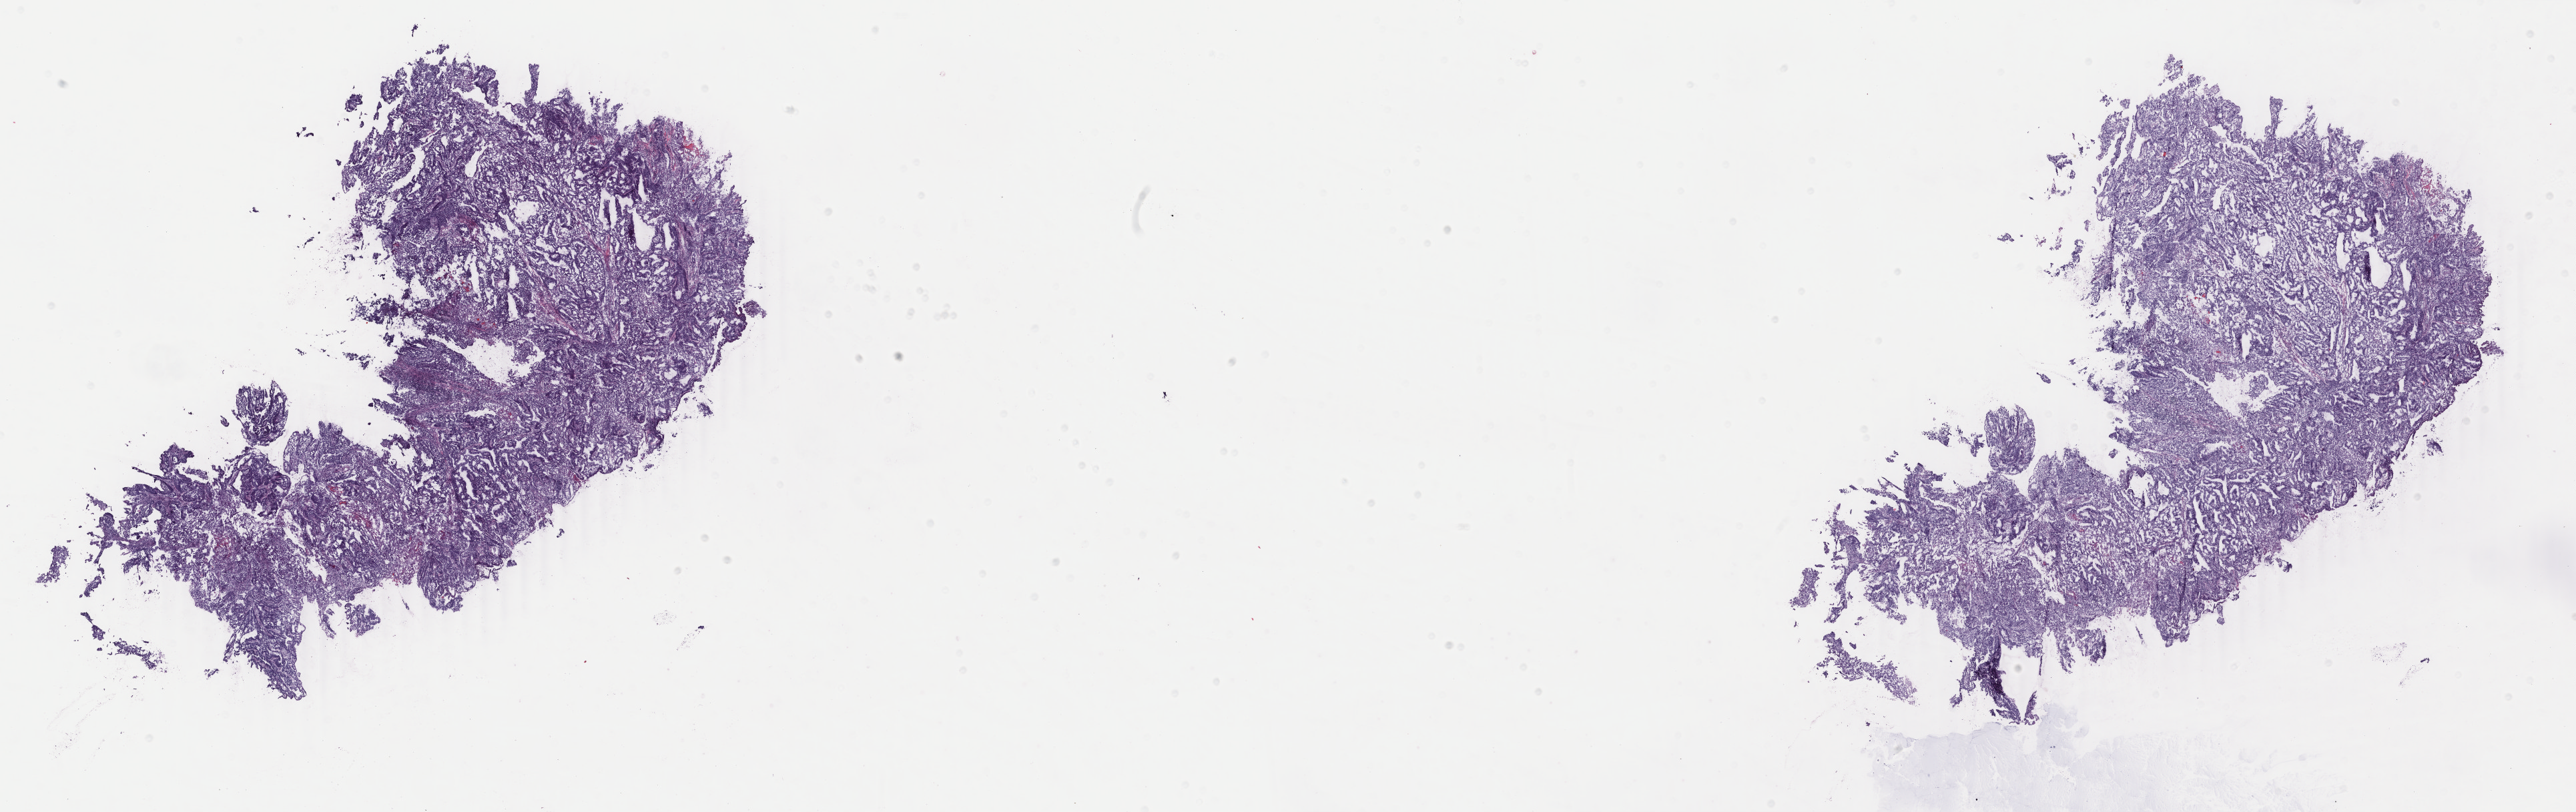
Digitized H&E-stained tissue section (whole slide) — shown as a low-resolution overview of the whole scanned area (about 30.7 x 9.7 mm, from a 40x scan). Frozen section. Uterus, primary tumour sample. Female patient; age at initial diagnosis 56 years.
Histologic diagnosis: Endometrioid adenocarcinoma, NOS (endometrium).